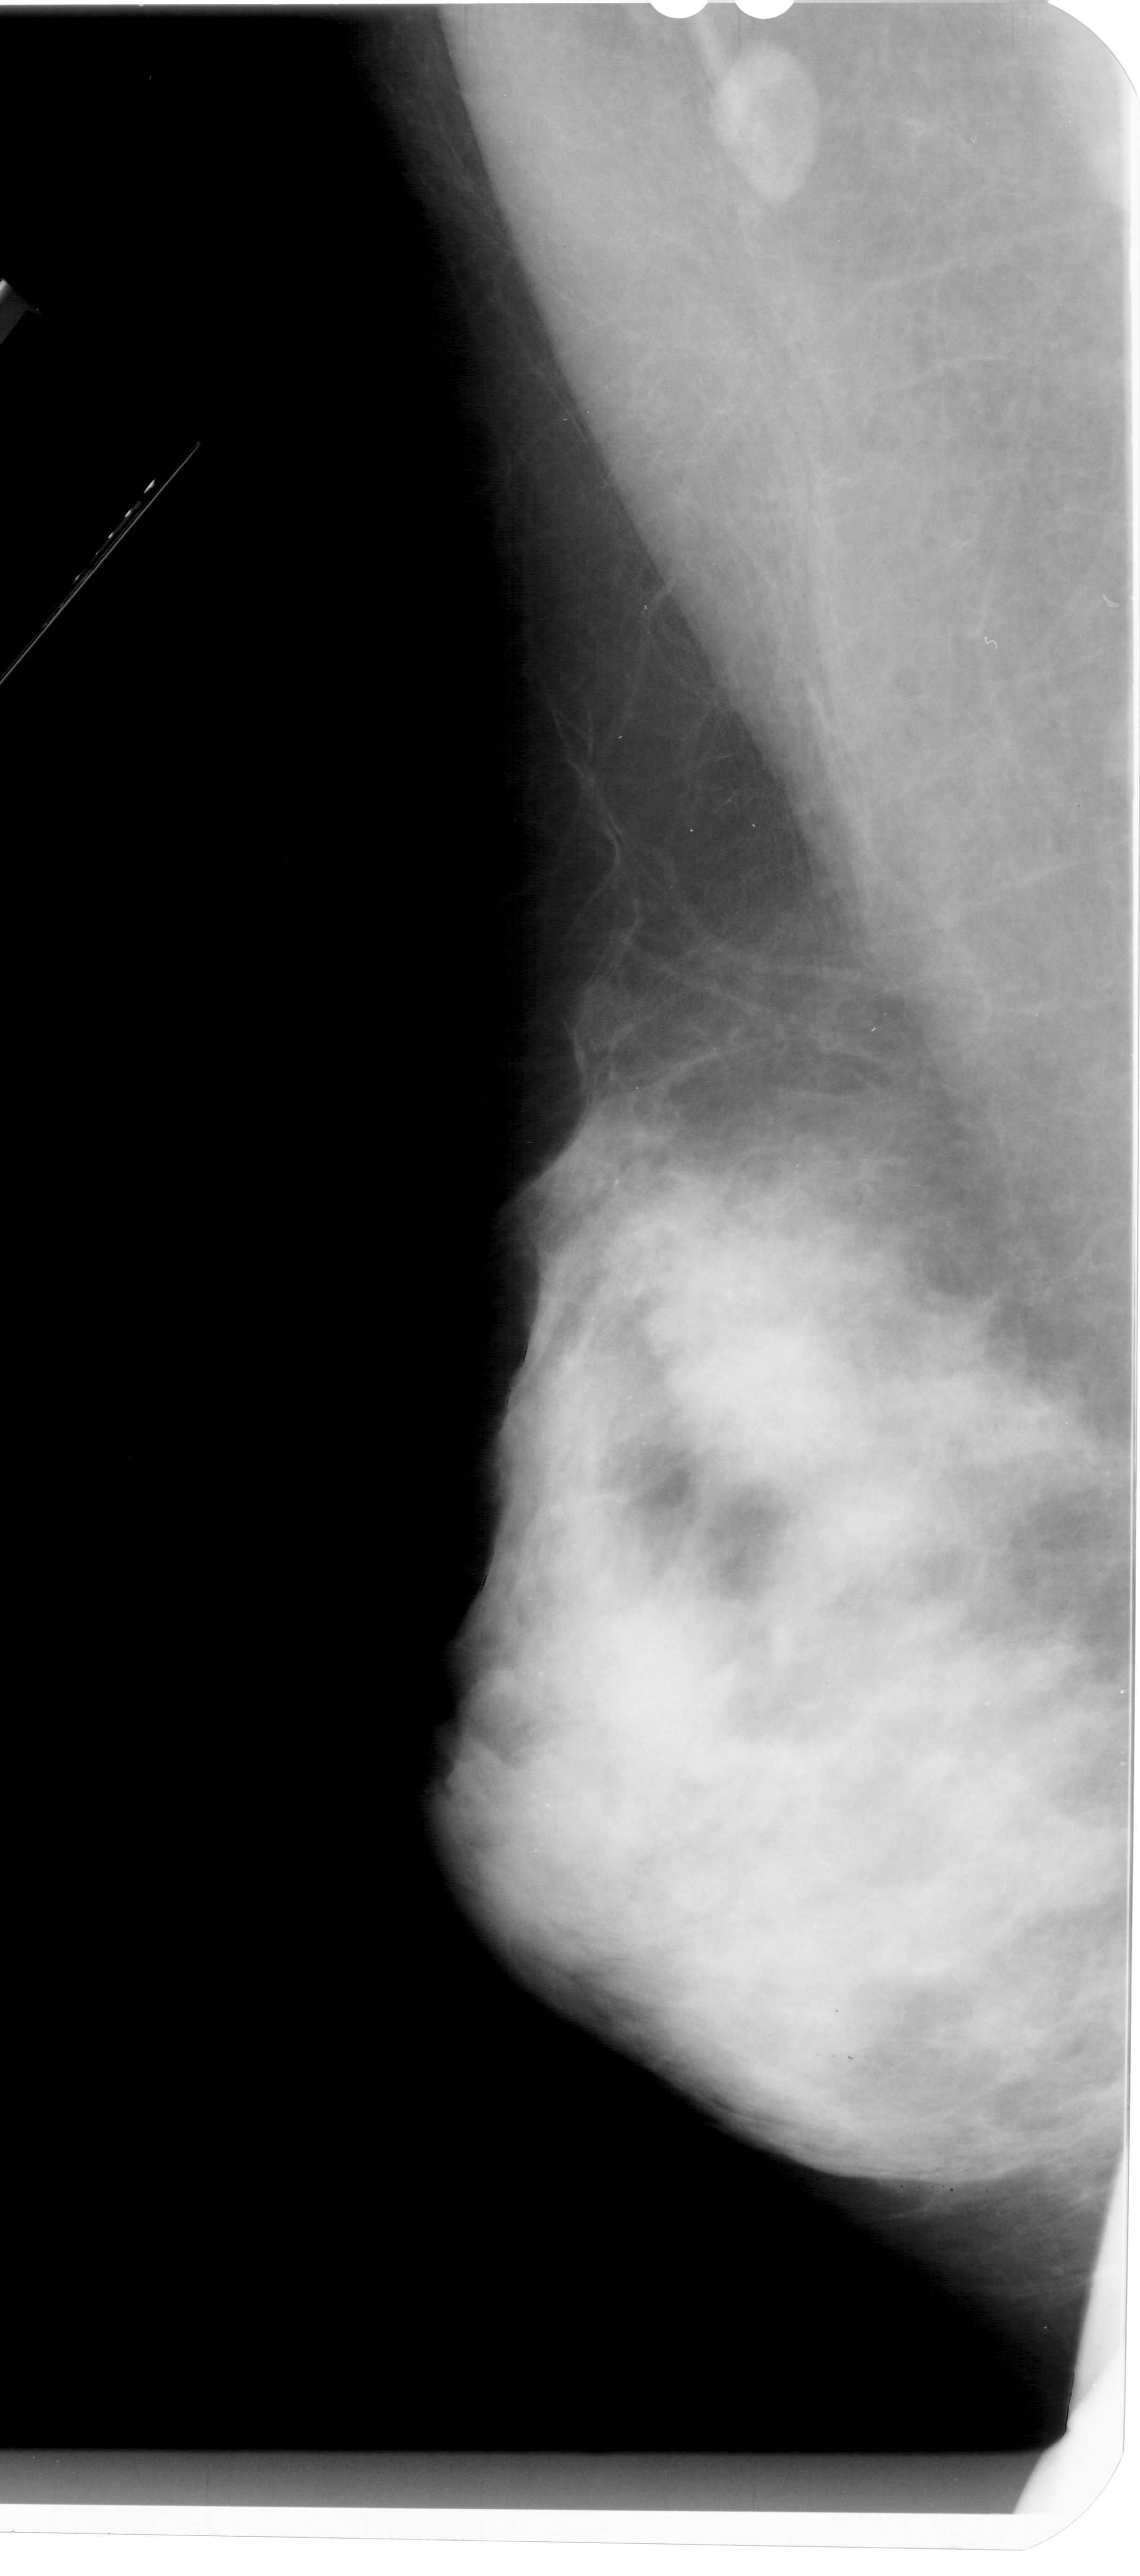
Scanned film-screen mammogram; left breast; mediolateral oblique (MLO) view; BI-RADS breast density category 4 (scale 1–4).
Calcifications, morphology punctate, distribution segmental; BI-RADS assessment category 4; subtlety rating 2 on a 1 (subtle) to 5 (obvious) scale; pathology result (as recorded, not read from the image): malignant.